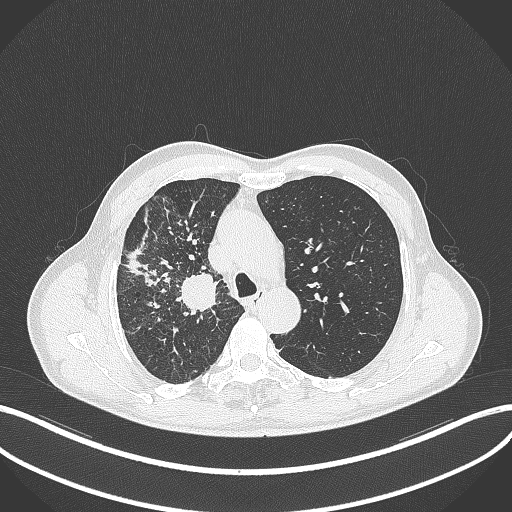
Chest CT, one axial slice. Slice 346 of 490 in the series (ordered by position). Lung window (W 1500 / L -600 HU). 1 mm slice thickness. 512 × 512 image matrix. Patient: male, 69 years. Case-level facts recorded for this patient, not image findings: clinical TNM (as recorded): T2a N0 M0.
Annotated regions visible in this slice (bounding box drawn by a radiologist):
- lung tumour (recorded histology: adenocarcinoma): bounding box (x1, y1, x2, y2) in pixels: (180, 271, 221, 312)